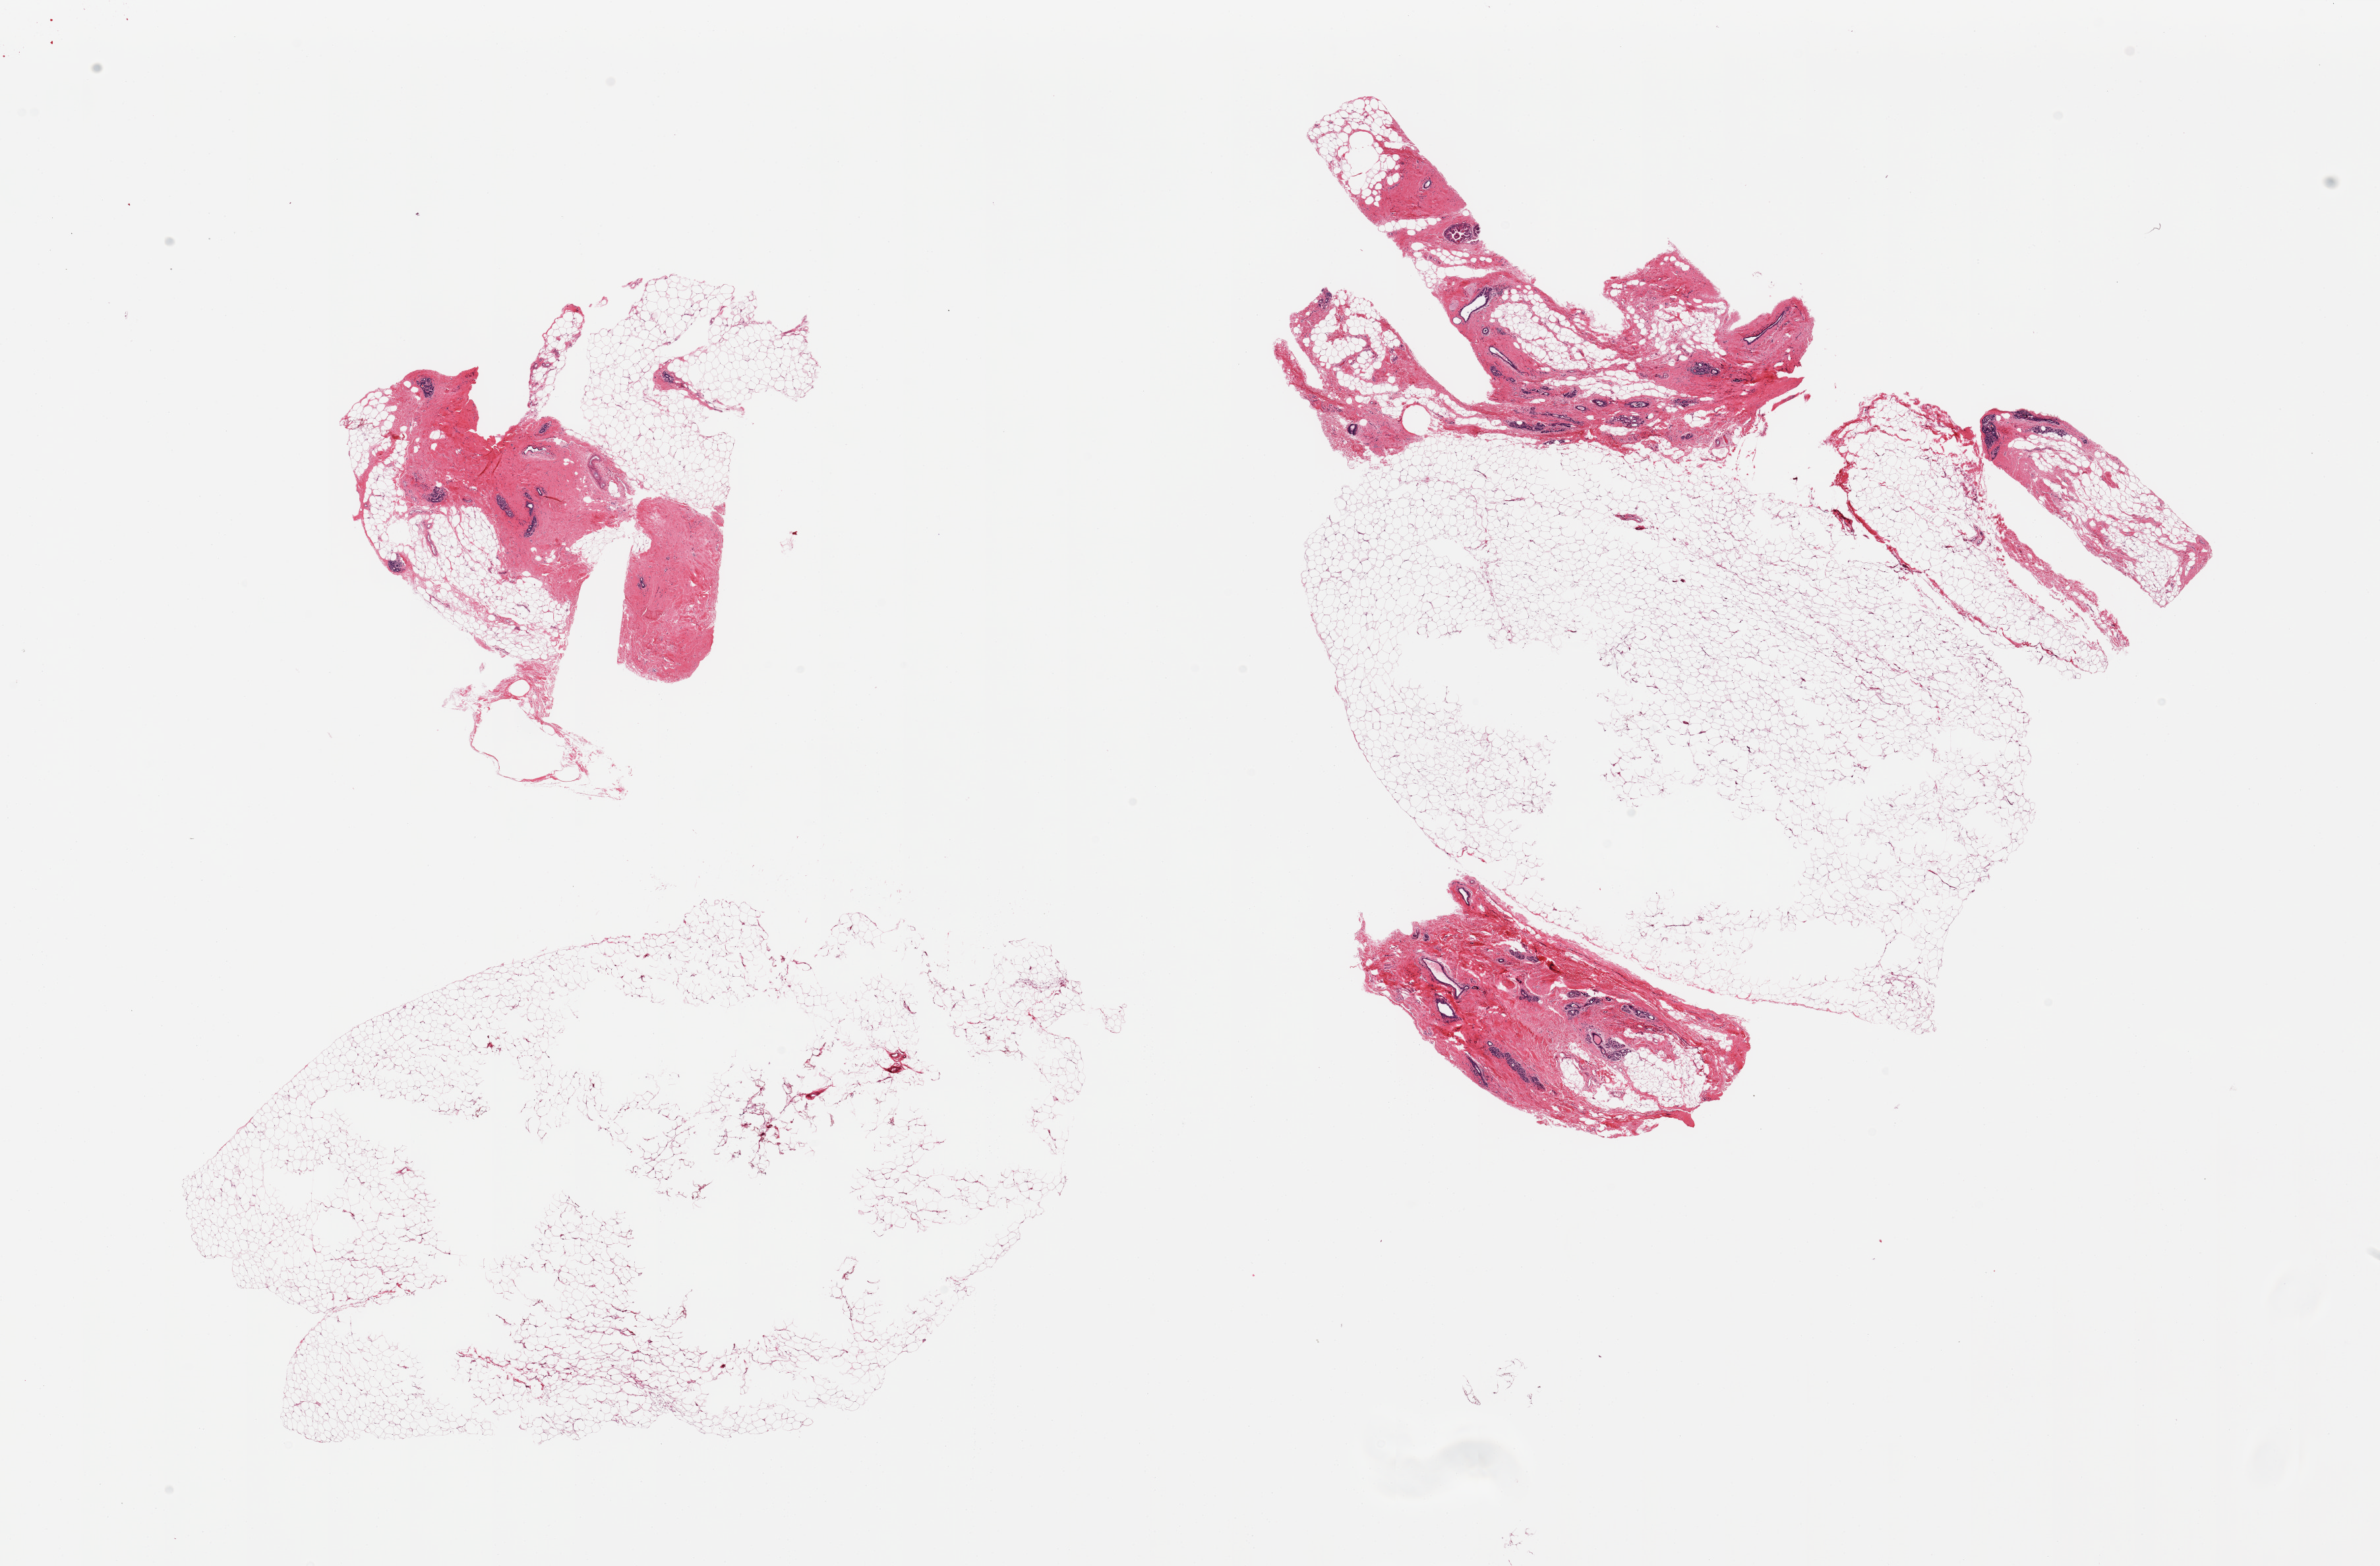
Whole-slide image, H&E stain, a low-resolution overview of the entire scanned area, about 28.5 x 18.8 mm, PAXgene-fixed, paraffin-embedded tissue, section of breast (target tissue), tissue donor sample.
Pathologist's review note for this sample: 3 pieces, post menopausal atophy.